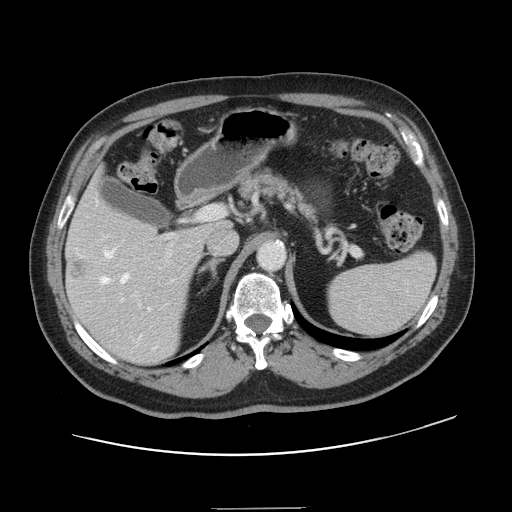
Contrast-enhanced abdominal CT, one axial slice. 120 kVp. Intravenous contrast given. Soft-tissue window (W 400 / L 40 HU). 2.5 mm slice thickness. 512 × 512 image matrix, field of view 402 × 402 mm. Male patient, age 62 years. From the clinical record (not read from this slice): diagnosis: colorectal cancer liver metastases, imaged before liver resection; multiple liver metastases: yes.
Structures marked on this image (outlined manually by an expert reader):
- hepatic veins: bounding box [x1, y1, x2, y2] px = [101, 251, 151, 338]
- liver: [67, 175, 222, 363]
- planned liver remnant (the part of the liver to remain after resection): [69, 178, 221, 243]
- portal vein (with intrahepatic branches): [121, 206, 220, 302]
- liver metastasis: [69, 257, 90, 280]